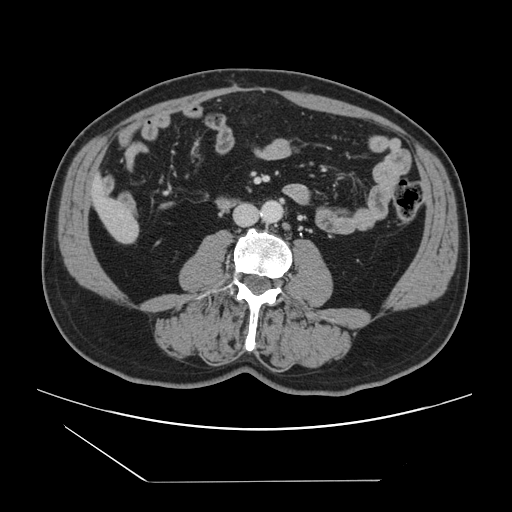
Contrast-enhanced abdominal CT, one axial slice. Slice 17 of 157 in the series (ordered by position). 120 kVp. Soft-tissue window (W 400 / L 40 HU). 2.5 mm slice thickness. 512 × 512 image matrix, field of view 407 × 407 mm. Male patient, age 61 years. Case-level facts recorded for this patient, not image findings: diagnosis: colorectal cancer liver metastases, imaged before liver resection; multiple liver metastases: yes; largest metastasis: 5.5 cm; chemotherapy before resection: no.
Structures marked on this image (expert manual segmentation):
- liver: bounding box (x1, y1, x2, y2) in pixels: (94, 182, 139, 243)
- planned liver remnant (the part of the liver to remain after resection): (94, 182, 121, 217)